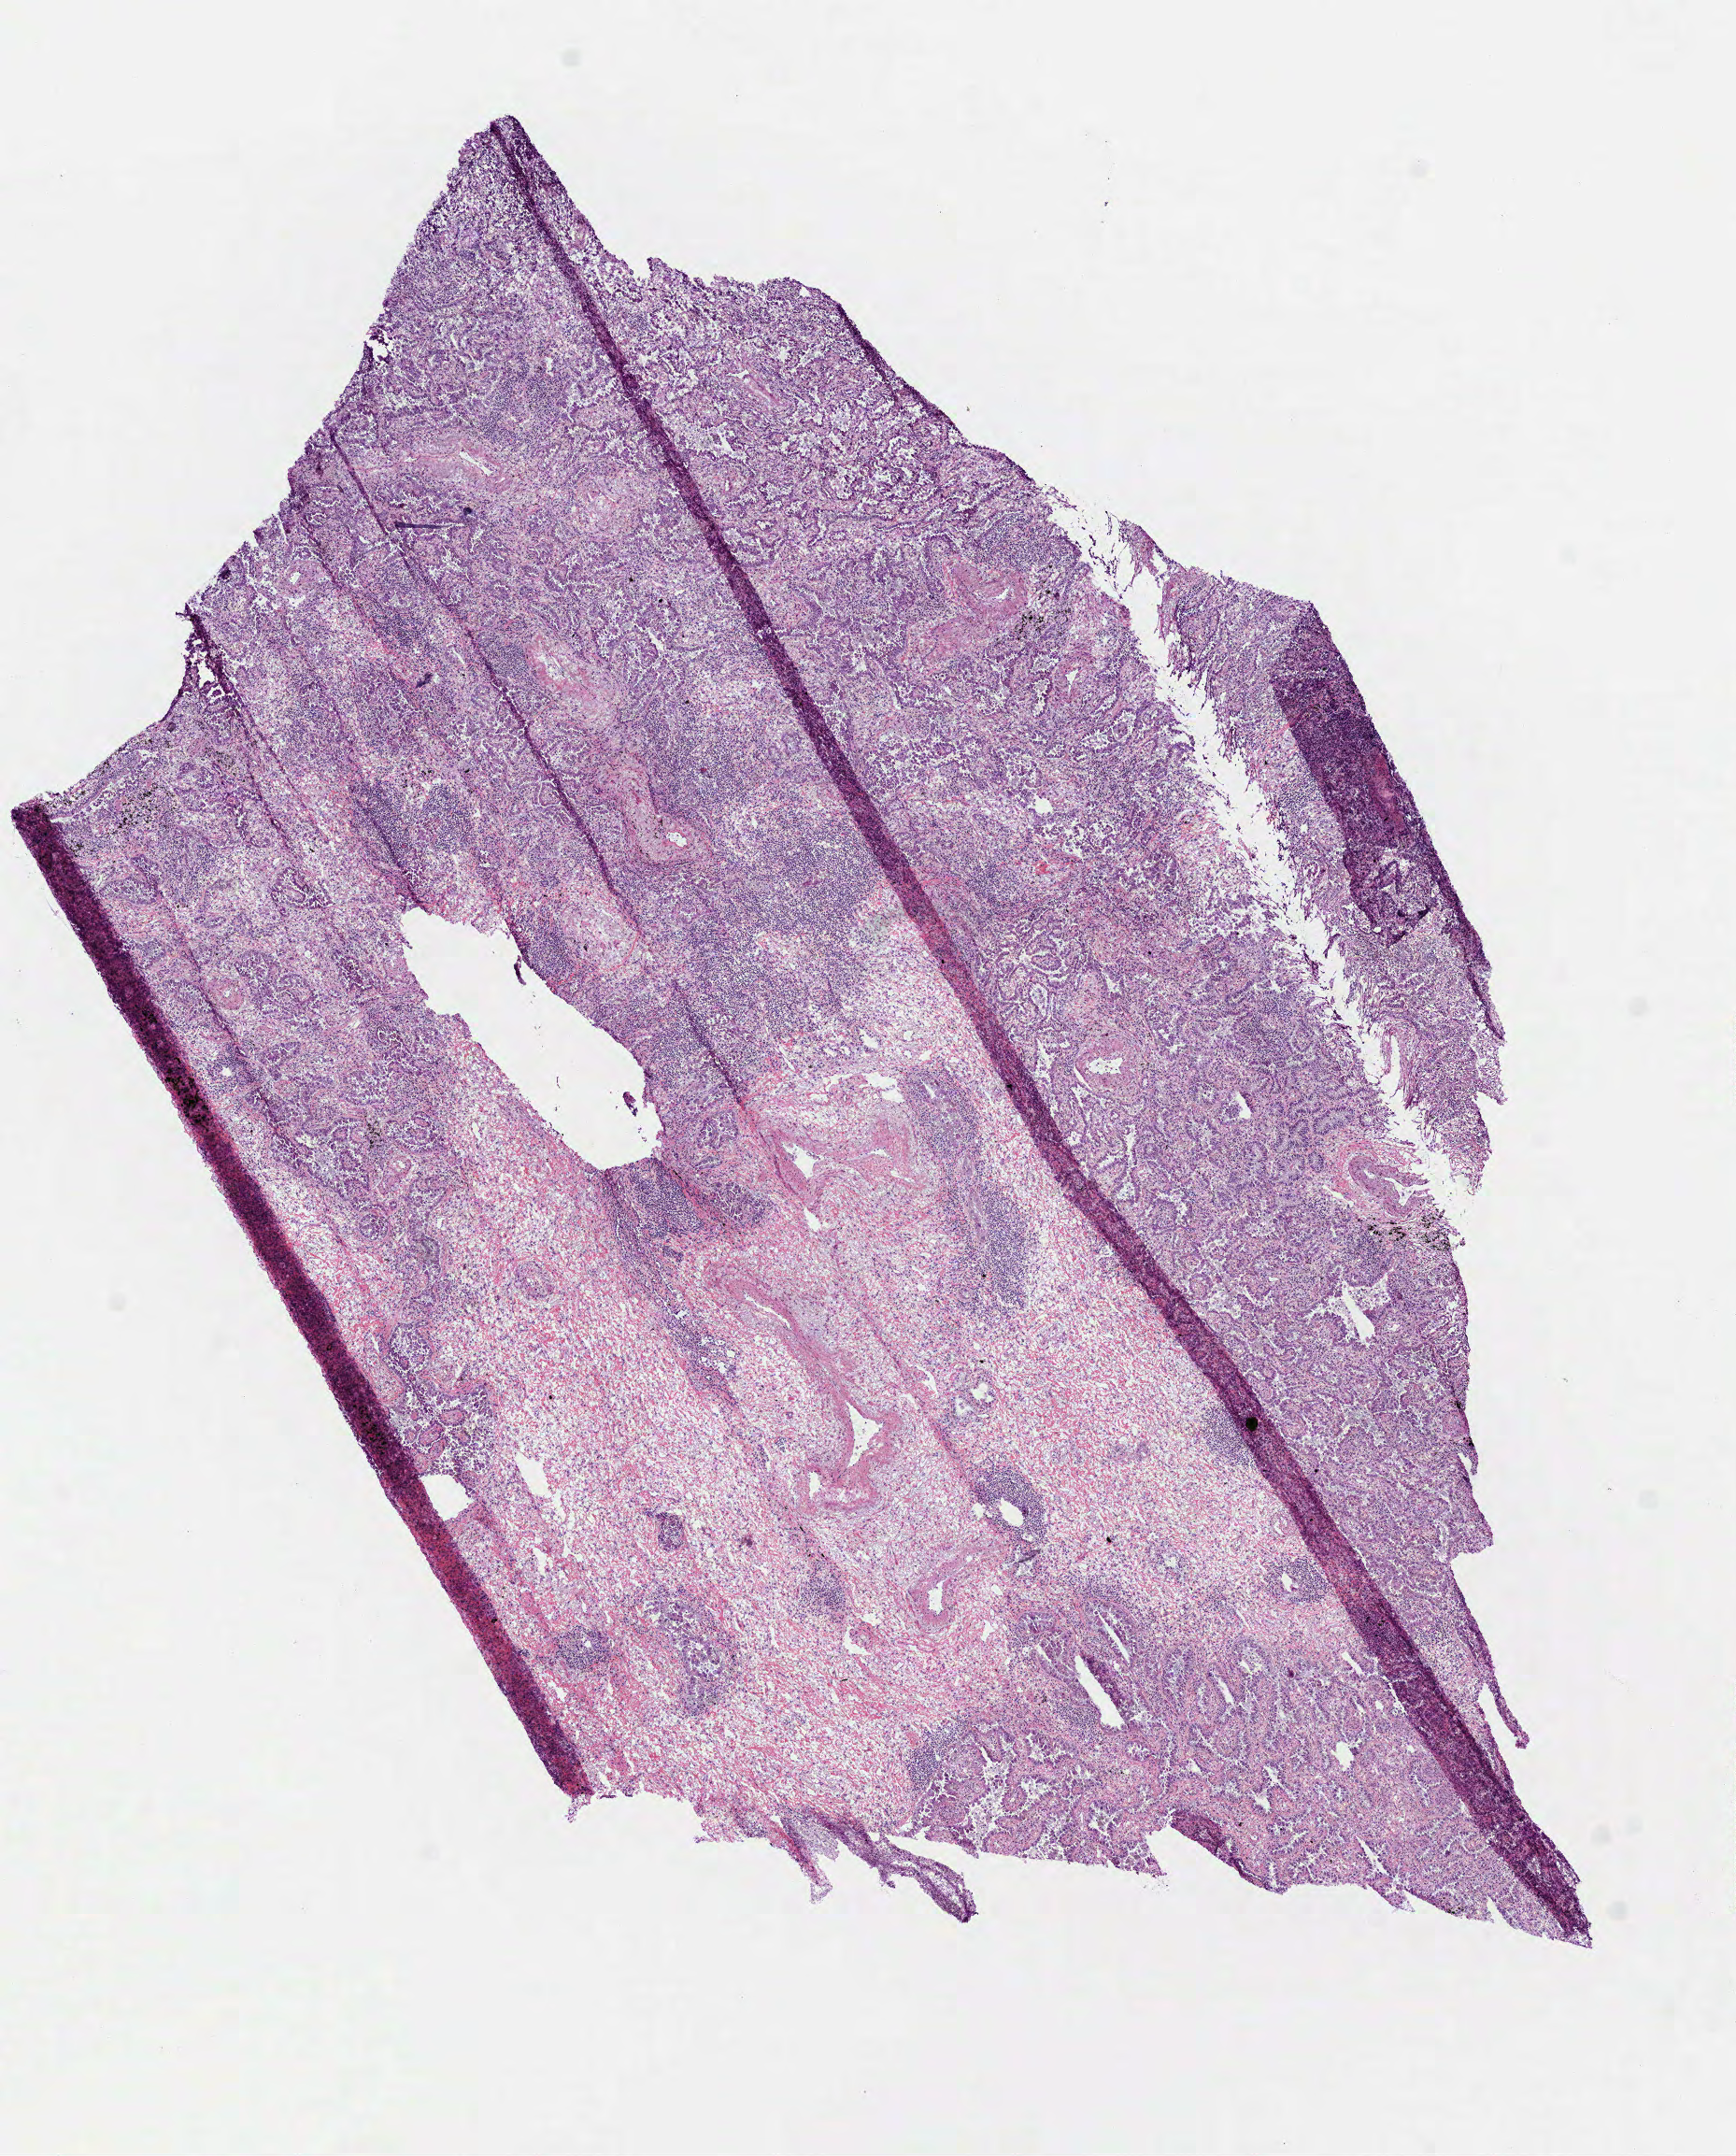
Digitized Hematoxylin and eosin (H&E) stained tissue section (whole slide), low-resolution overview of the scanned area, about 7.5 x 9.3 mm (from a 40x scan); frozen section from the bottom of the tissue portion; sample: primary tumour, lung. Patient: female, age at initial diagnosis 73 years.
Pathologic diagnosis: Adenocarcinoma, NOS.